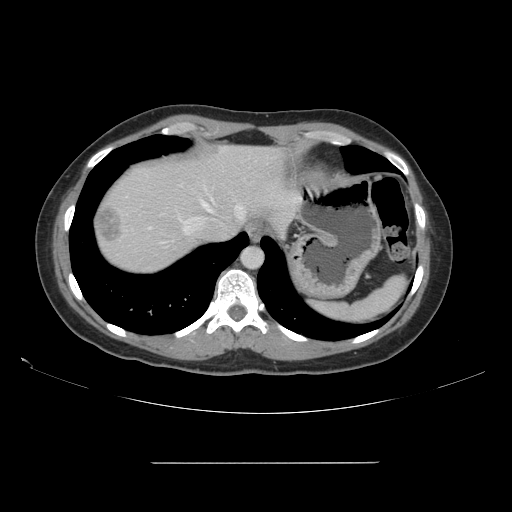
Contrast-enhanced abdominal CT, one axial slice; position 132 of 151 along the scan axis; soft-tissue window (W 400 / L 40 HU); 2.5 mm slice thickness; 512 × 512 image matrix, field of view 421 × 421 mm. Female patient, age 46 years. From the clinical record (not read from this slice): diagnosis: colorectal cancer liver metastases, imaged before liver resection; multiple liver metastases: yes; largest metastasis: 3 cm.
Annotated regions visible in this slice (outlined manually by an expert reader):
- hepatic veins: box from (x=184, y=201) to (x=244, y=233) px
- liver: (x=94, y=146)–(x=284, y=274)
- planned liver remnant (the part of the liver to remain after resection): (x=107, y=148)–(x=283, y=237)
- liver metastasis: (x=97, y=206)–(x=122, y=247)